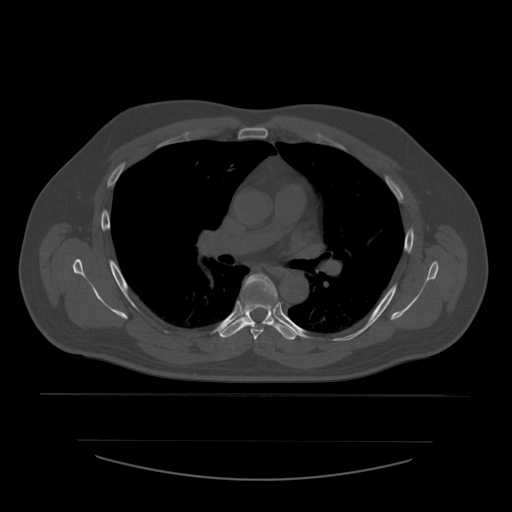
CT including the spine, one axial slice; slice 387 of 532 in the series (ordered by position); reconstruction kernel STANDARD; 120 kVp; bone window (W 1800 / L 400 HU); 1.25 mm slice thickness; 512 × 512 image matrix. Patient age 44 years. Case-level facts recorded for this patient, not image findings: primary cancer: soft tissue sarcoma.
Annotated regions visible in this slice (semi-automatically segmented with operator editing):
- T5 vertebra: bounding box <244,274,278,340> (left, top, right, bottom; pixels)
- T6 vertebra: <220,280,298,340>